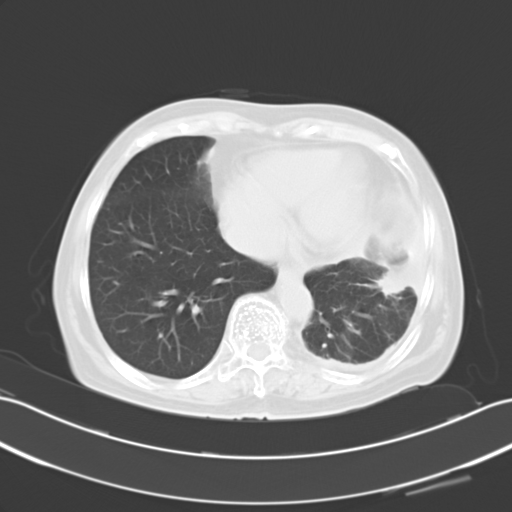
Chest CT, one axial slice; reconstruction kernel B40f; 120 kVp; lung window (W 1500 / L -600 HU); 10 mm slice thickness; 512 × 512 image matrix. Patient: female, 82 years. From the clinical record (not read from this slice): clinical TNM (as recorded): T1c N0 M1.
Annotated regions visible in this slice (rectangle marked by the reading radiologist):
- lung tumour (recorded histology: adenocarcinoma): bounding box (x1, y1, x2, y2) in pixels: (376, 257, 416, 301)